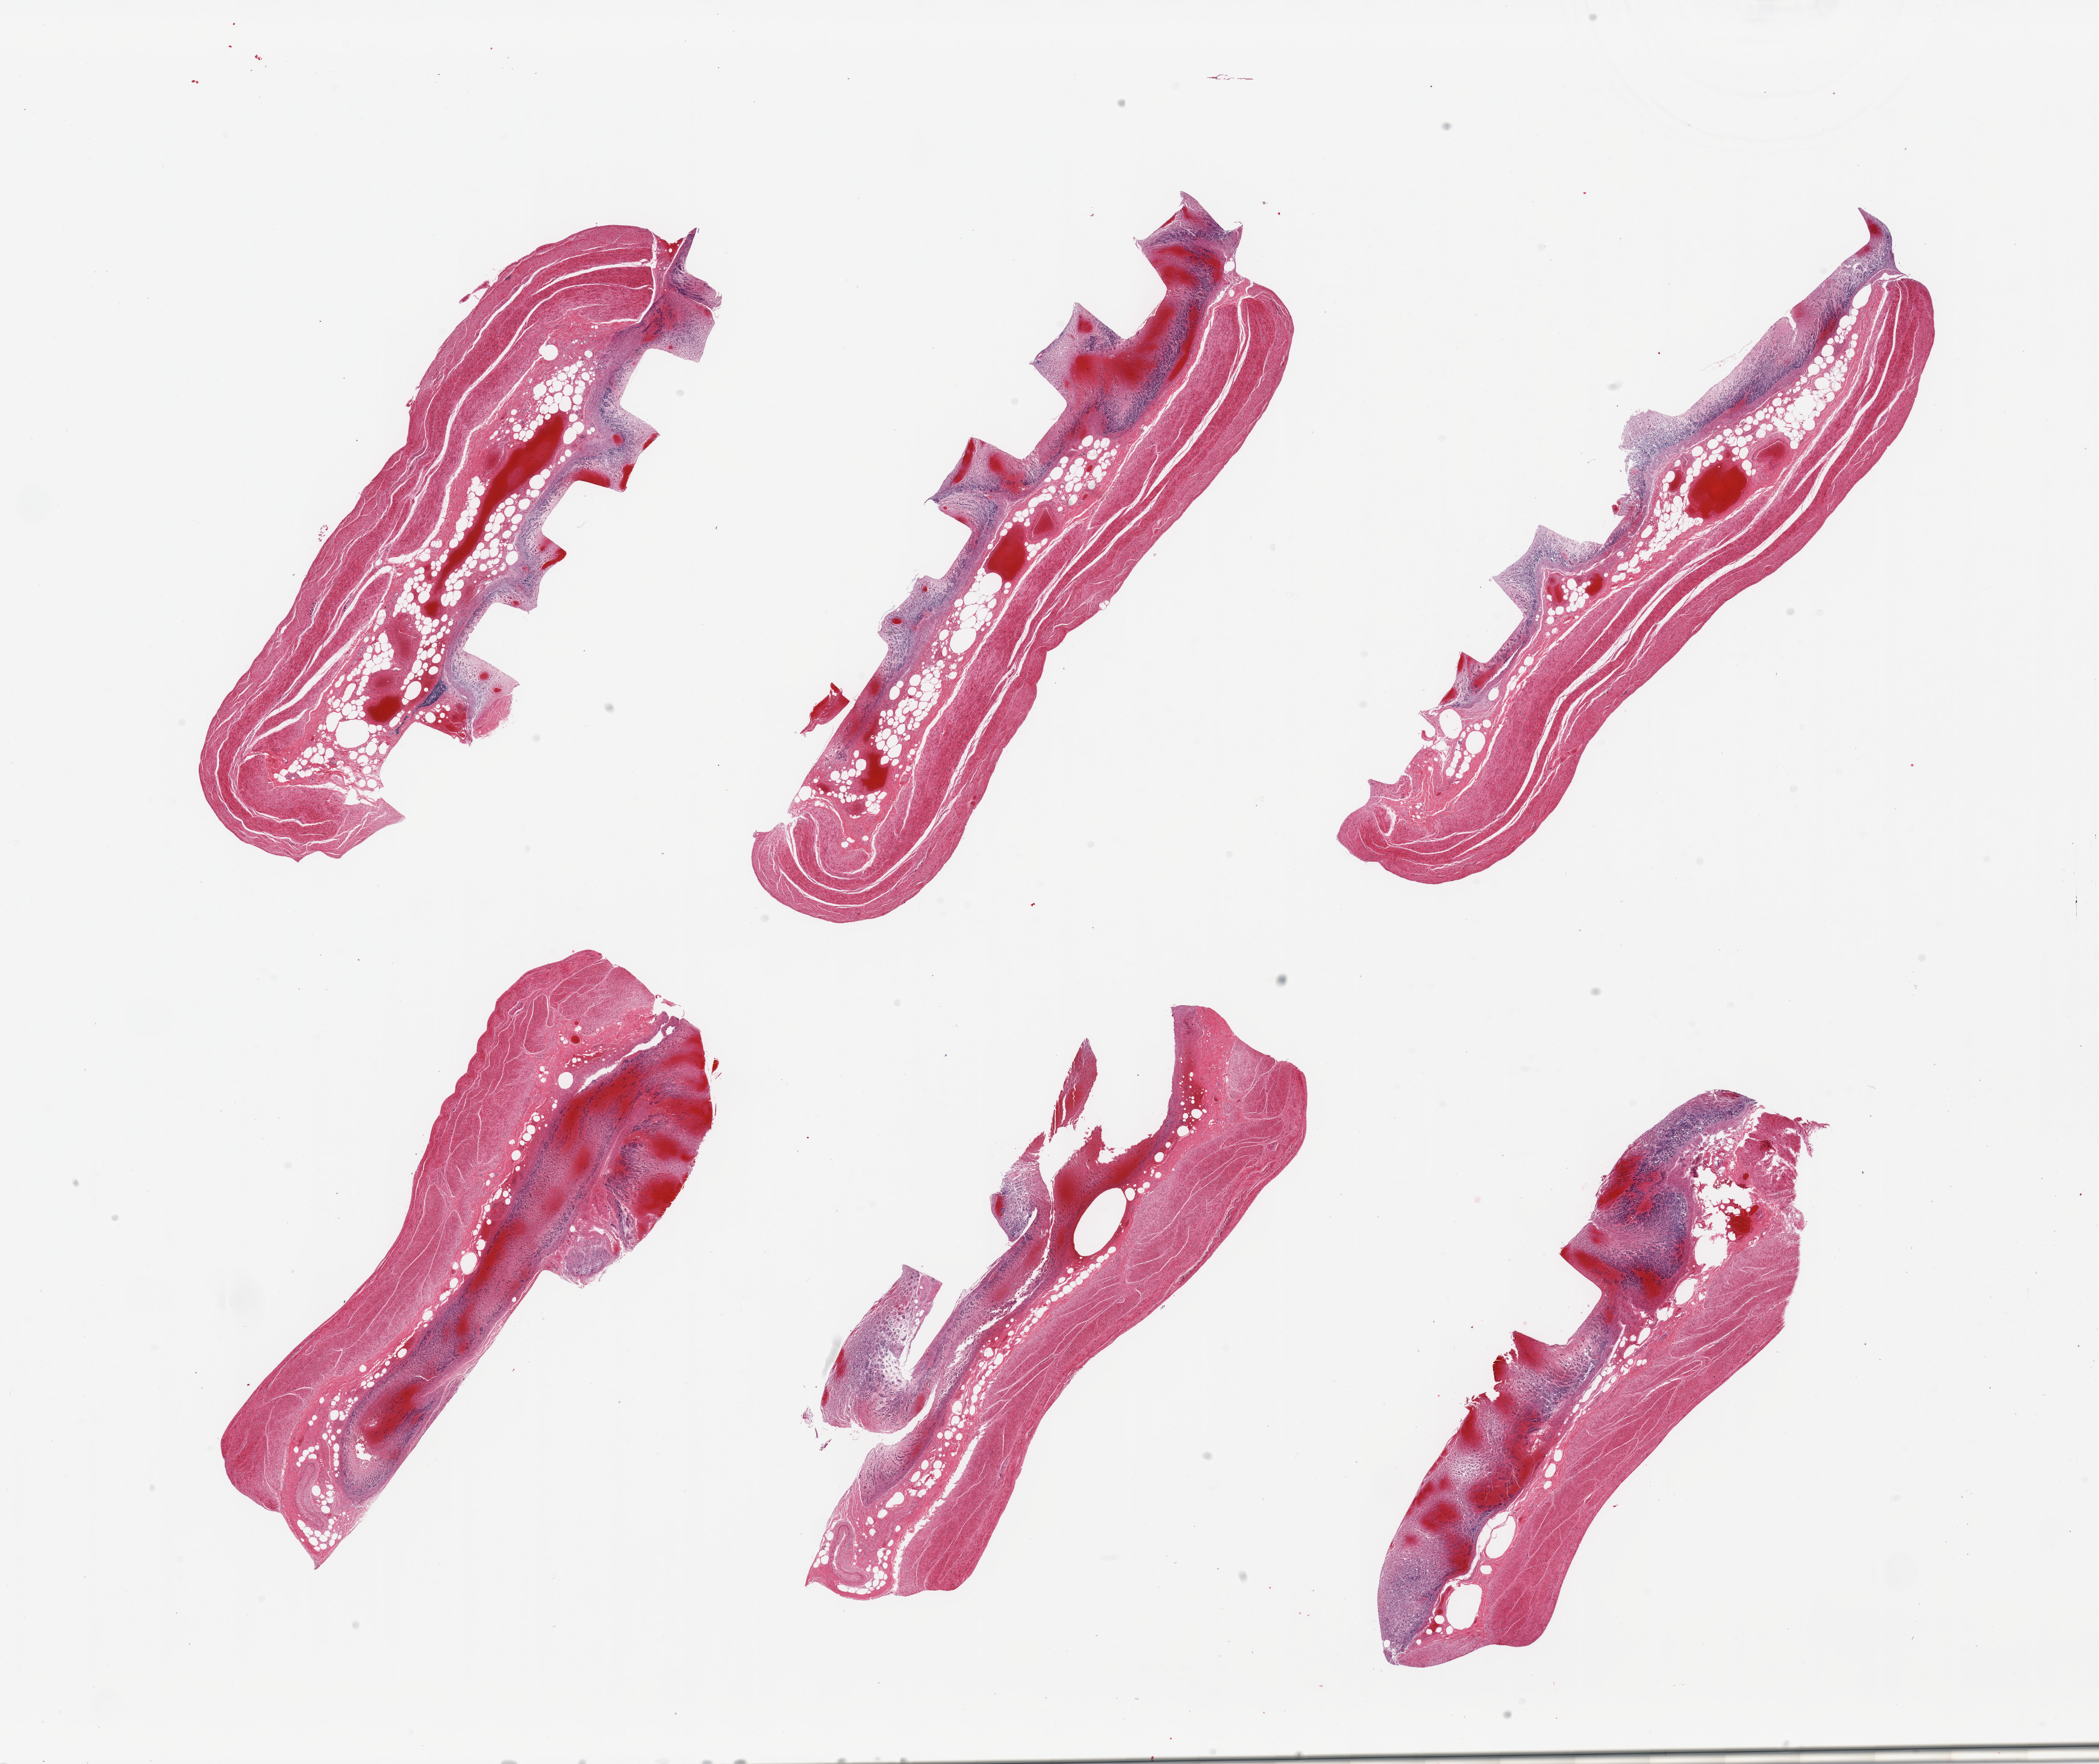
Whole-slide image, haematoxylin and eosin stain, a low-resolution overview of the entire scanned area, about 27.6 x 23.2 mm (from a 20x scan), PAXgene-fixed, paraffin-embedded tissue, target tissue: stomach, donor tissue sample.
Pathologist's review note for this sample: 6 pieces, target mucosa up to ~0.5mm but with advanced autolysis/sloughing.